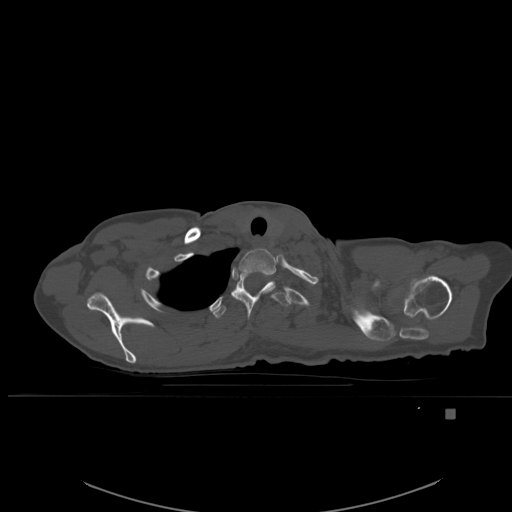
CT including the spine, one axial slice; position 439 of 537 along the scan axis; bone window (W 1800 / L 400 HU); 512 × 512 image matrix. Female patient, age 45 years. Case-level facts recorded for this patient, not image findings: primary cancer: lung.
Annotated regions visible in this slice (semi-automatic segmentation, software-assisted and operator-edited):
- T1 vertebra: box from (x=235, y=248) to (x=276, y=279) px
- T2 vertebra: (x=231, y=275)–(x=290, y=320)
- T3 vertebra: (x=212, y=302)–(x=227, y=319)